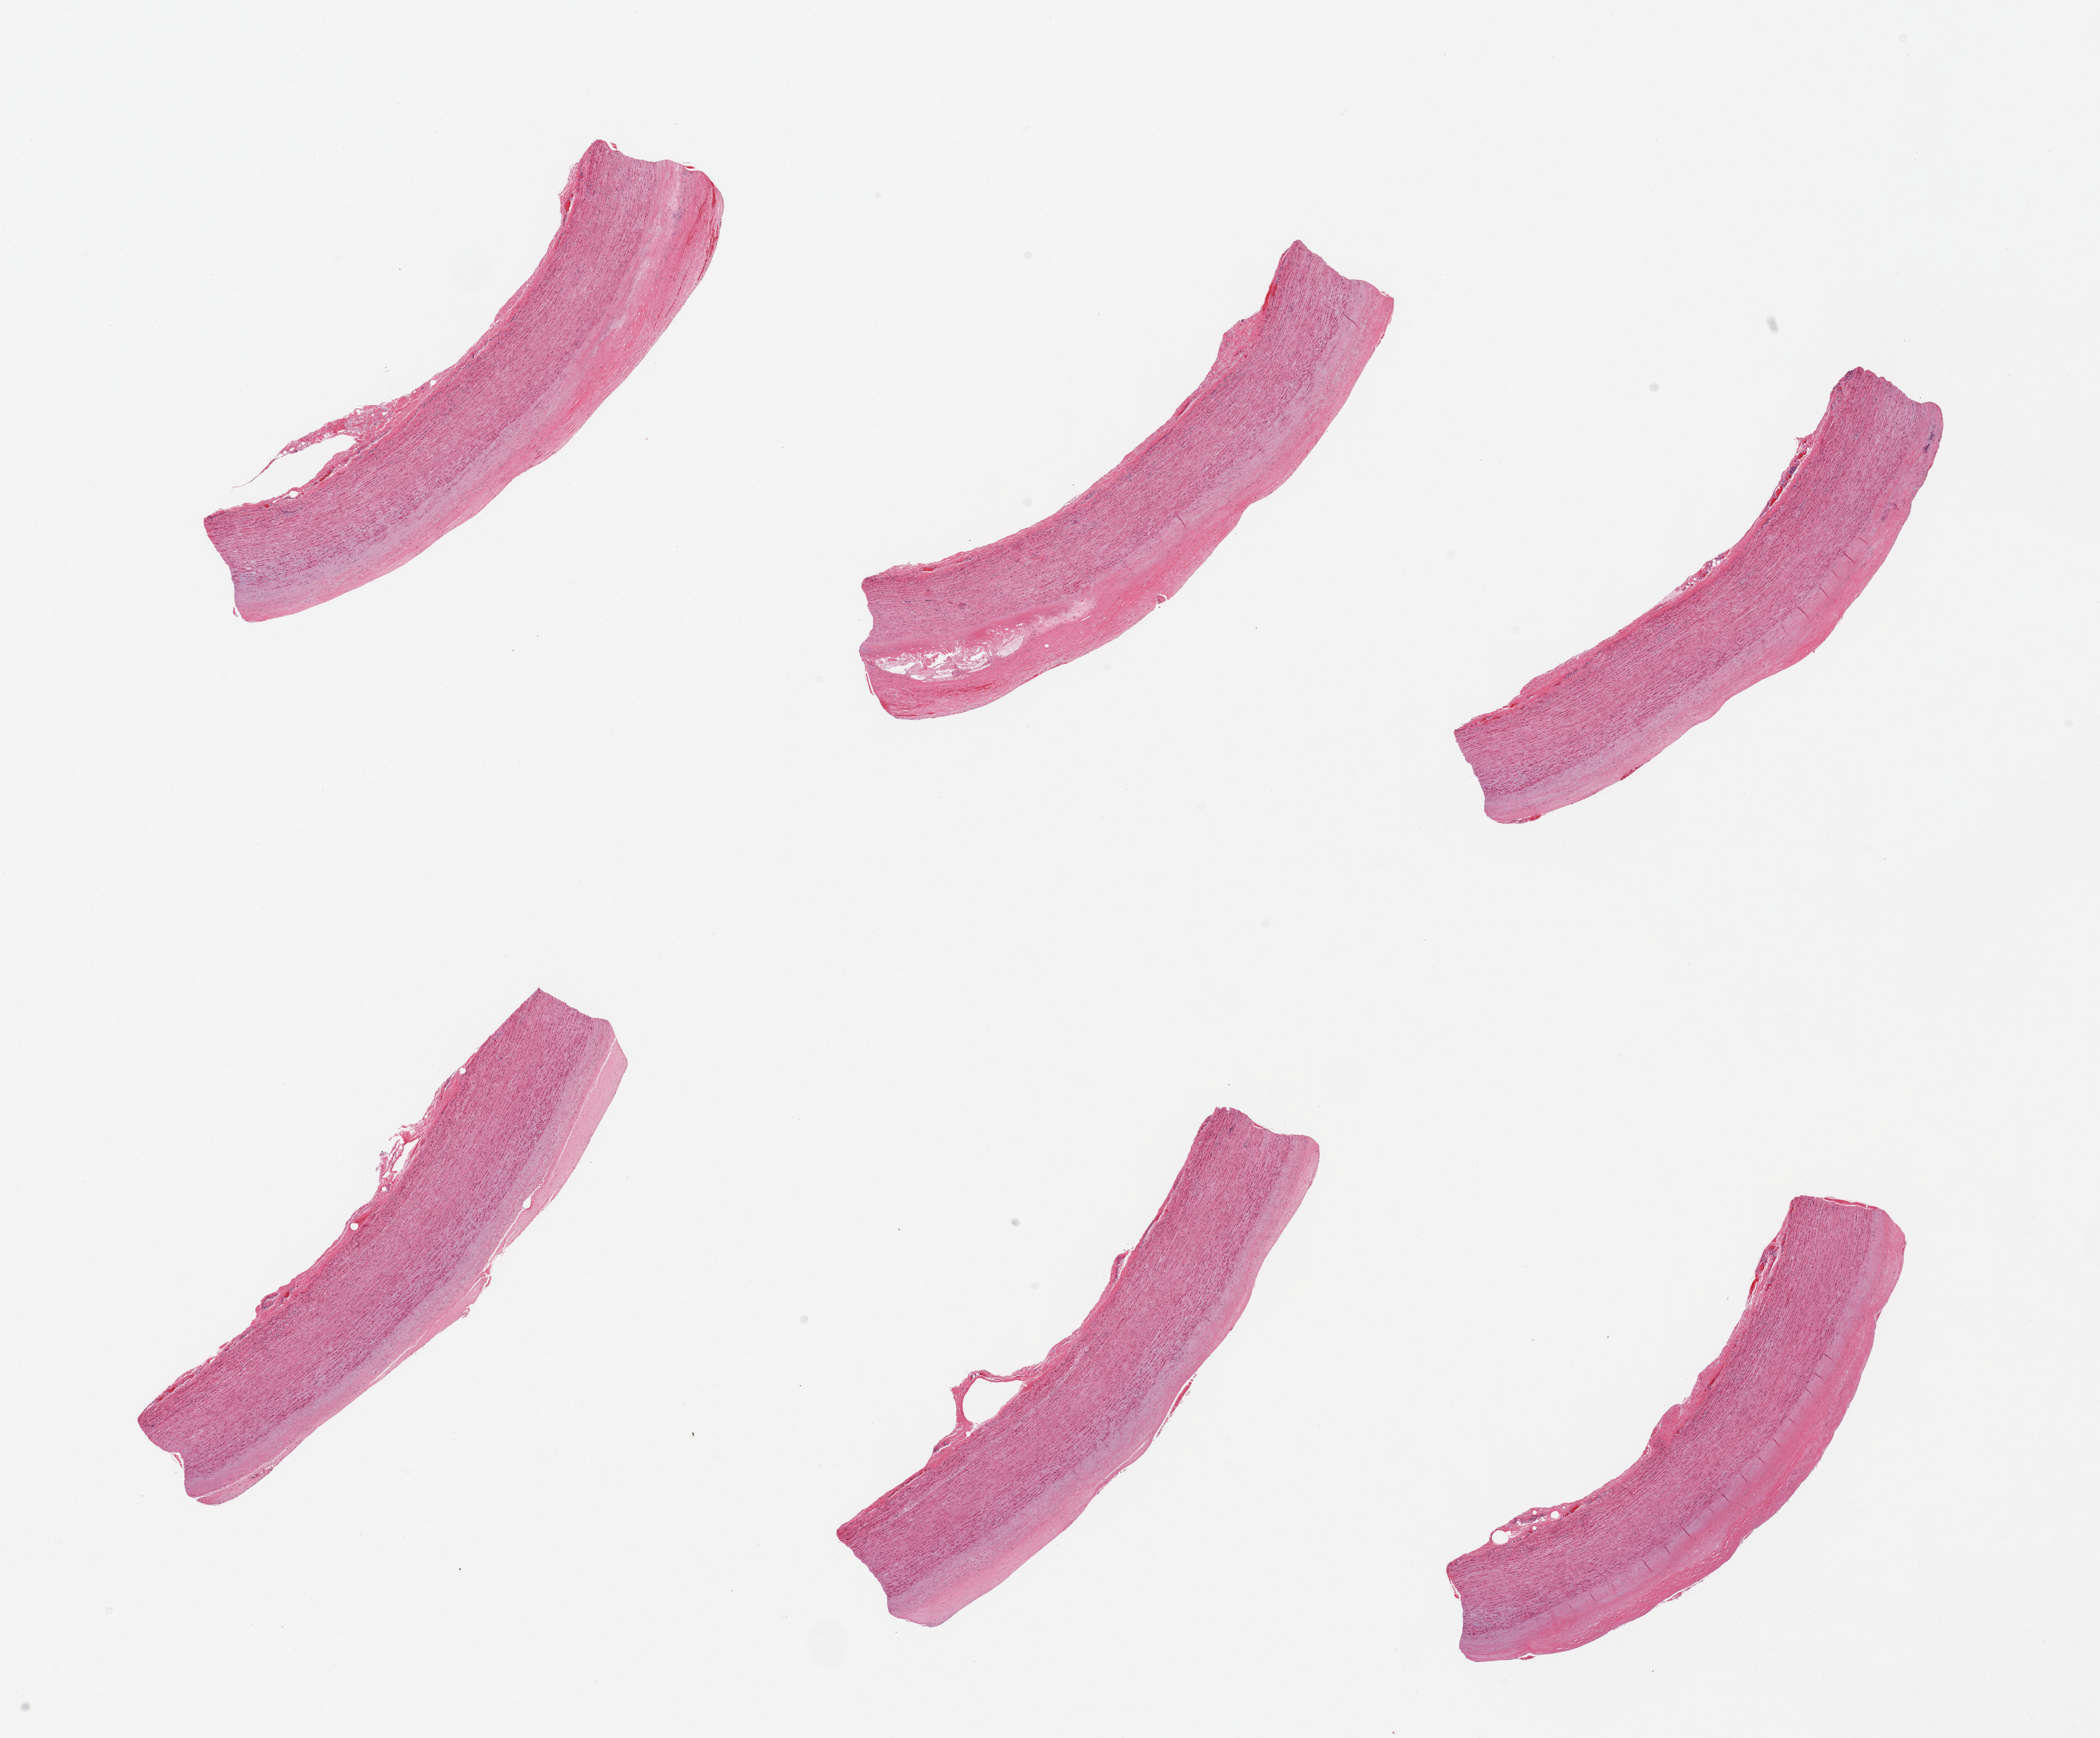
Digitized haematoxylin and eosin-stained section, brightfield — shown as a low-resolution overview of the whole scanned area (about 23.6 x 19.6 mm, acquisition: 20x scan). PAXgene-fixed, paraffin-embedded tissue. Section of aorta (target tissue). Donor tissue sample. Donor: male.
- pathologist's review note for this sample: 6 pieces, athoerosis up to ~0.75mm